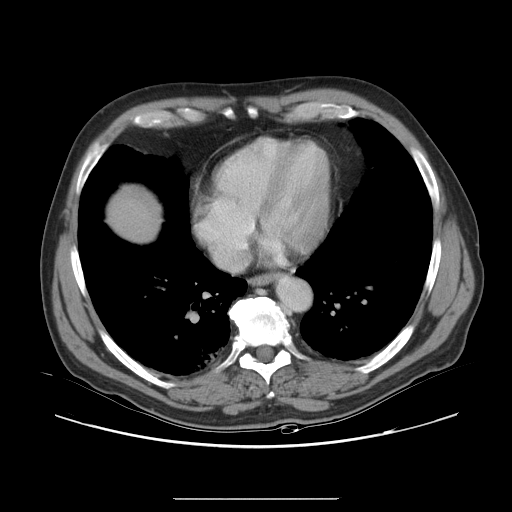
Contrast-enhanced abdominal CT, one axial slice. Position 33 of 40 along the scan axis. 120 kVp. Intravenous contrast given. Soft-tissue window (W 400 / L 40 HU). 5 mm slice thickness. 512 × 512 image matrix, field of view 408 × 408 mm. Male patient, age 64 years. Case-level facts recorded for this patient, not image findings: diagnosis: colorectal cancer liver metastases, imaged before liver resection; multiple liver metastases: yes; largest metastasis: 3.2 cm; chemotherapy before resection: yes.
Annotated regions visible in this slice (manually delineated by an expert):
- liver: bounding box (x1, y1, x2, y2) in pixels: (110, 188, 157, 241)
- planned liver remnant (the part of the liver to remain after resection): (110, 188, 158, 241)